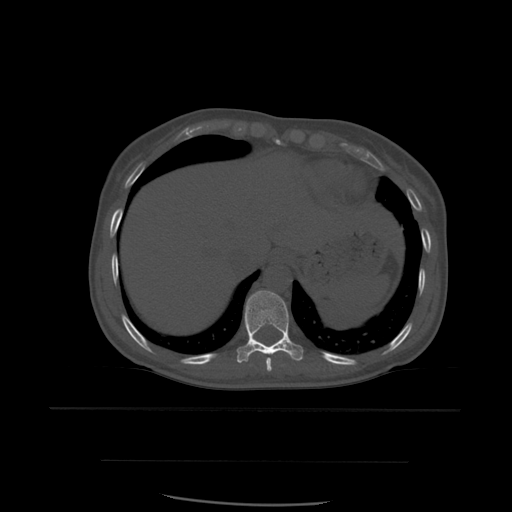
CT including the spine, one axial slice; position 318 of 574 along the scan axis; bone window (W 1800 / L 400 HU); 1.25 mm slice thickness; 512 × 512 image matrix, field of view 392 × 392 mm. Patient age 48 years. From the clinical record (not read from this slice): primary cancer: lung.
Outlined on this slice (semi-automatically segmented with operator editing):
- T10 vertebra: bounding box [x1, y1, x2, y2] px = [237, 290, 304, 363]
- T9 vertebra: [266, 354, 273, 372]